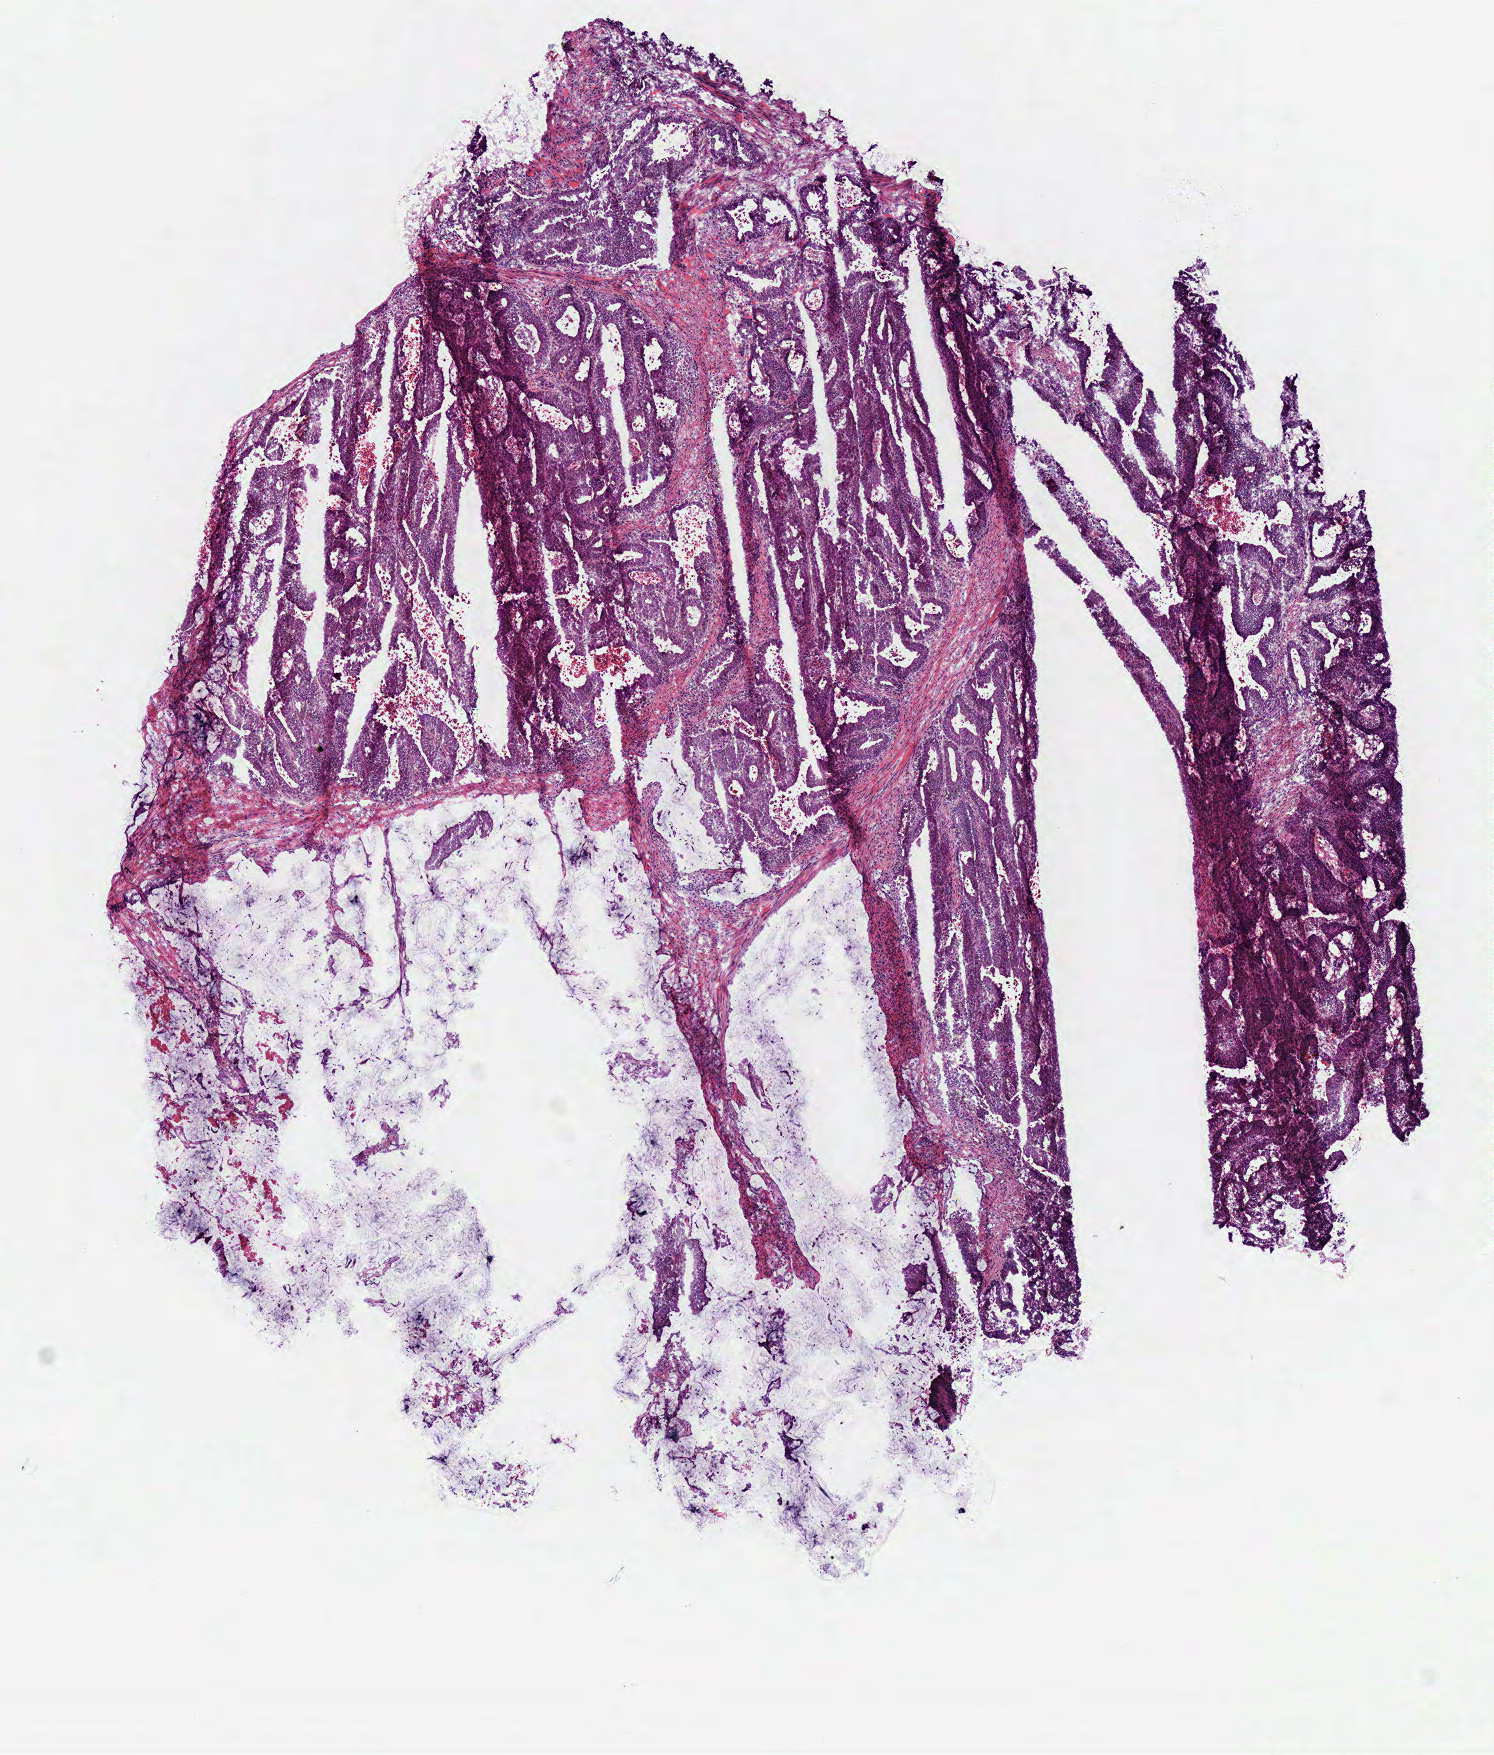
Digitized H&E-stained tissue section (whole slide), low-resolution overview of the scanned area, about 5.9 x 6.9 mm (slide scanned at 40x); frozen section; sample: primary tumour, colon. Female, age 79 years at initial diagnosis. Pathologist review of this section (percent, as recorded): tumour cells 75%, tumour nuclei 70%, normal cells 0%, stromal cells 10%, necrosis 15%.
• AJCC pathologic stage: I (7th edition)
• histologic diagnosis: Mucinous adenocarcinoma (cecum)